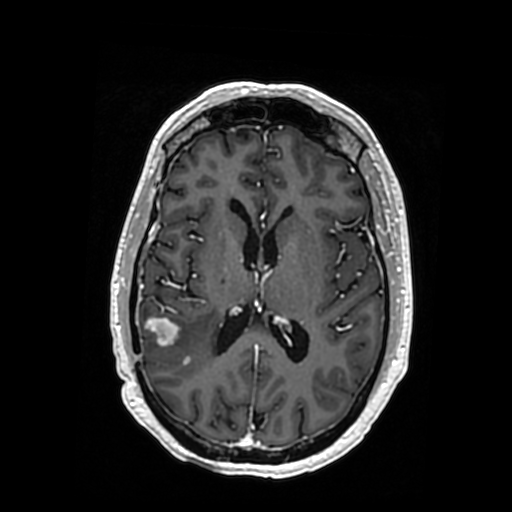
Brain MRI from a brain-tumour surgery series, one axial slice. Slice 168 of 364 in the series (ordered by position). T1-weighted post-contrast. 0.5 mm slice thickness. 512 × 512 image matrix, field of view 260 × 260 mm. From the clinical record (not read from this slice): histopathology: Oligodendroglioma; WHO grade: 3; IDH mutation: yes; tumour location: Right Posterior Temporal Inferior Parietal.
Structures marked on this image (outlined manually by an expert reader):
- tumour: bounding box (x1, y1, x2, y2) in pixels: (146, 317, 217, 363)